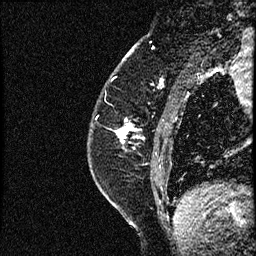
Breast MRI (dynamic contrast-enhanced), one sagittal slice. Slice 17 of 52 in the series (ordered by position). Dynamic contrast-enhanced study with each time point stored as its own series, time point 2 of 3 at this slice position (early post-contrast, ordered by acquisition time). 1.5 T. TE 4.2 ms, TR 17.6 ms. 256 × 256 image matrix. Patient: female, 49 years. From the clinical record (not read from this slice): setting: breast cancer imaged before/during neoadjuvant chemotherapy; receptor status: HER2-positive.
Structures marked on this image (semi-automatic segmentation, software-assisted and operator-edited):
- analysis volume of interest (the breast-tissue region the enhancement analysis was run in; not a lesion): bounding box (x1, y1, x2, y2) in pixels: (88, 65, 182, 175)
- tumour enhancement mask (voxels above the 100 % enhancement threshold inside the analysis volume of interest): (117, 124, 137, 139)